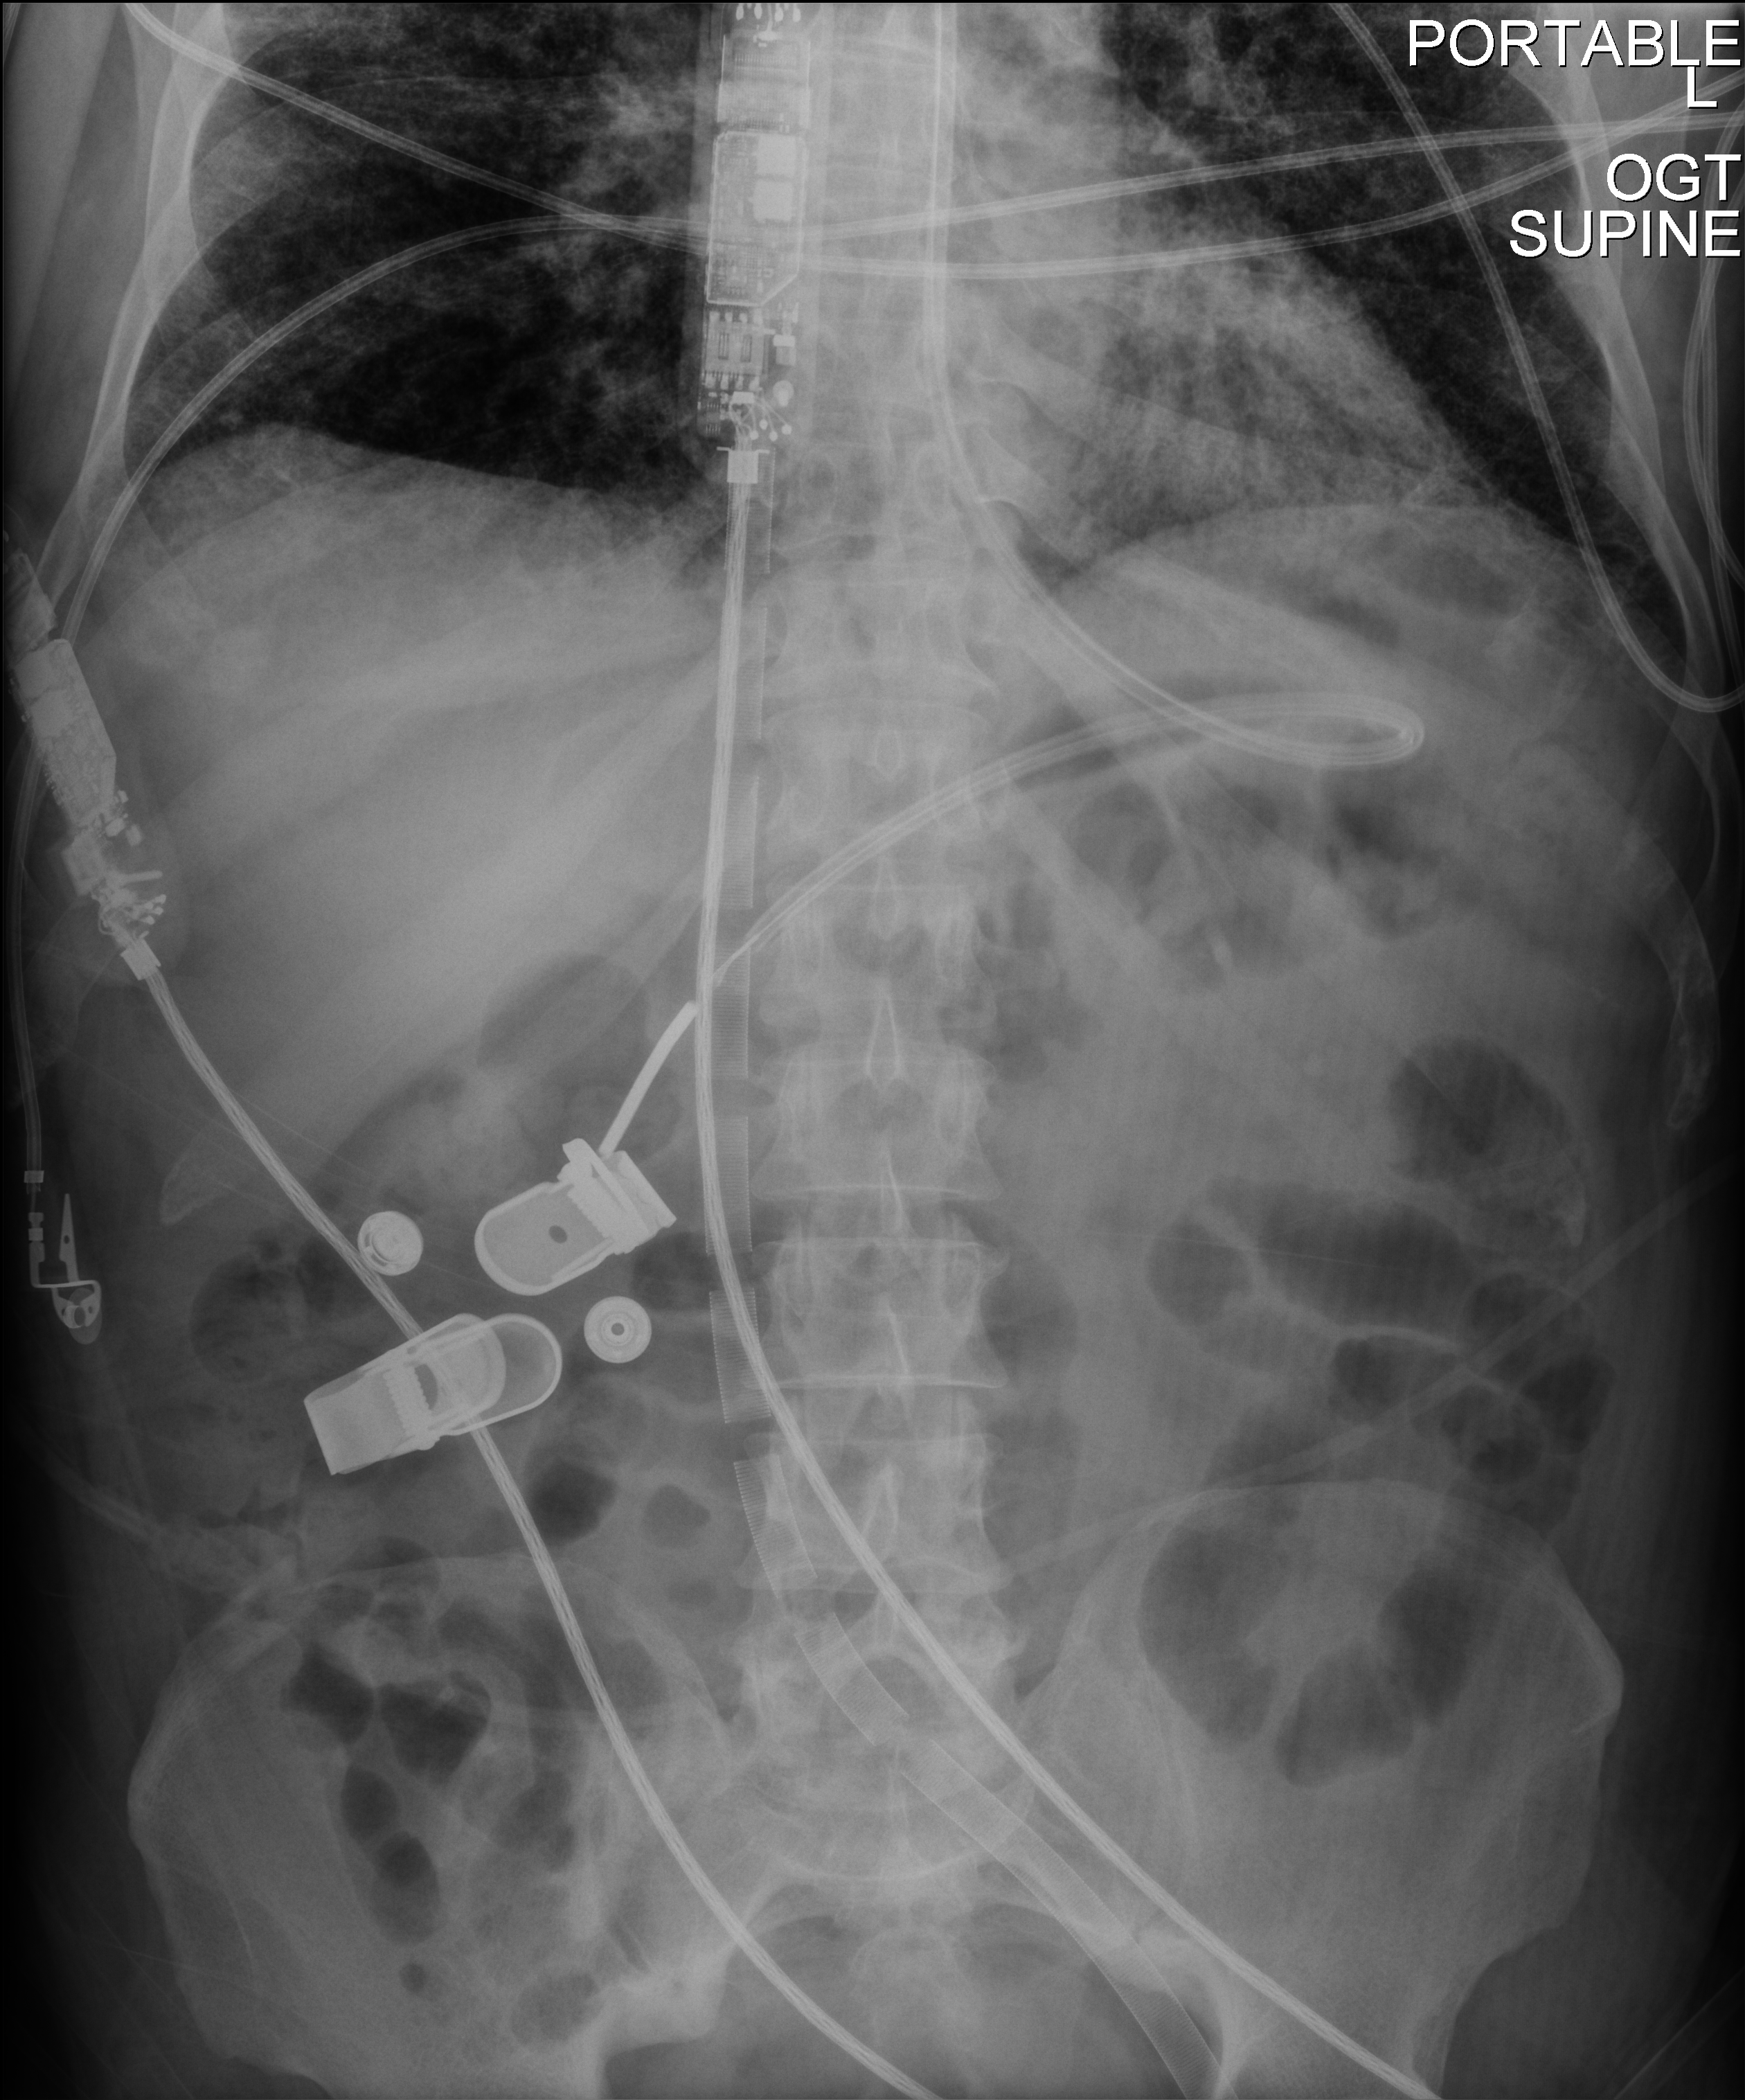
Abdomen radiograph, anteroposterior (AP) projection. Patient hospitalised with COVID-19; male, aged 18–59 years.
Hospital-stay facts (about this admission, not read from this image; timing relative to this image not recorded): admitted to intensive care during this hospital stay: yes.